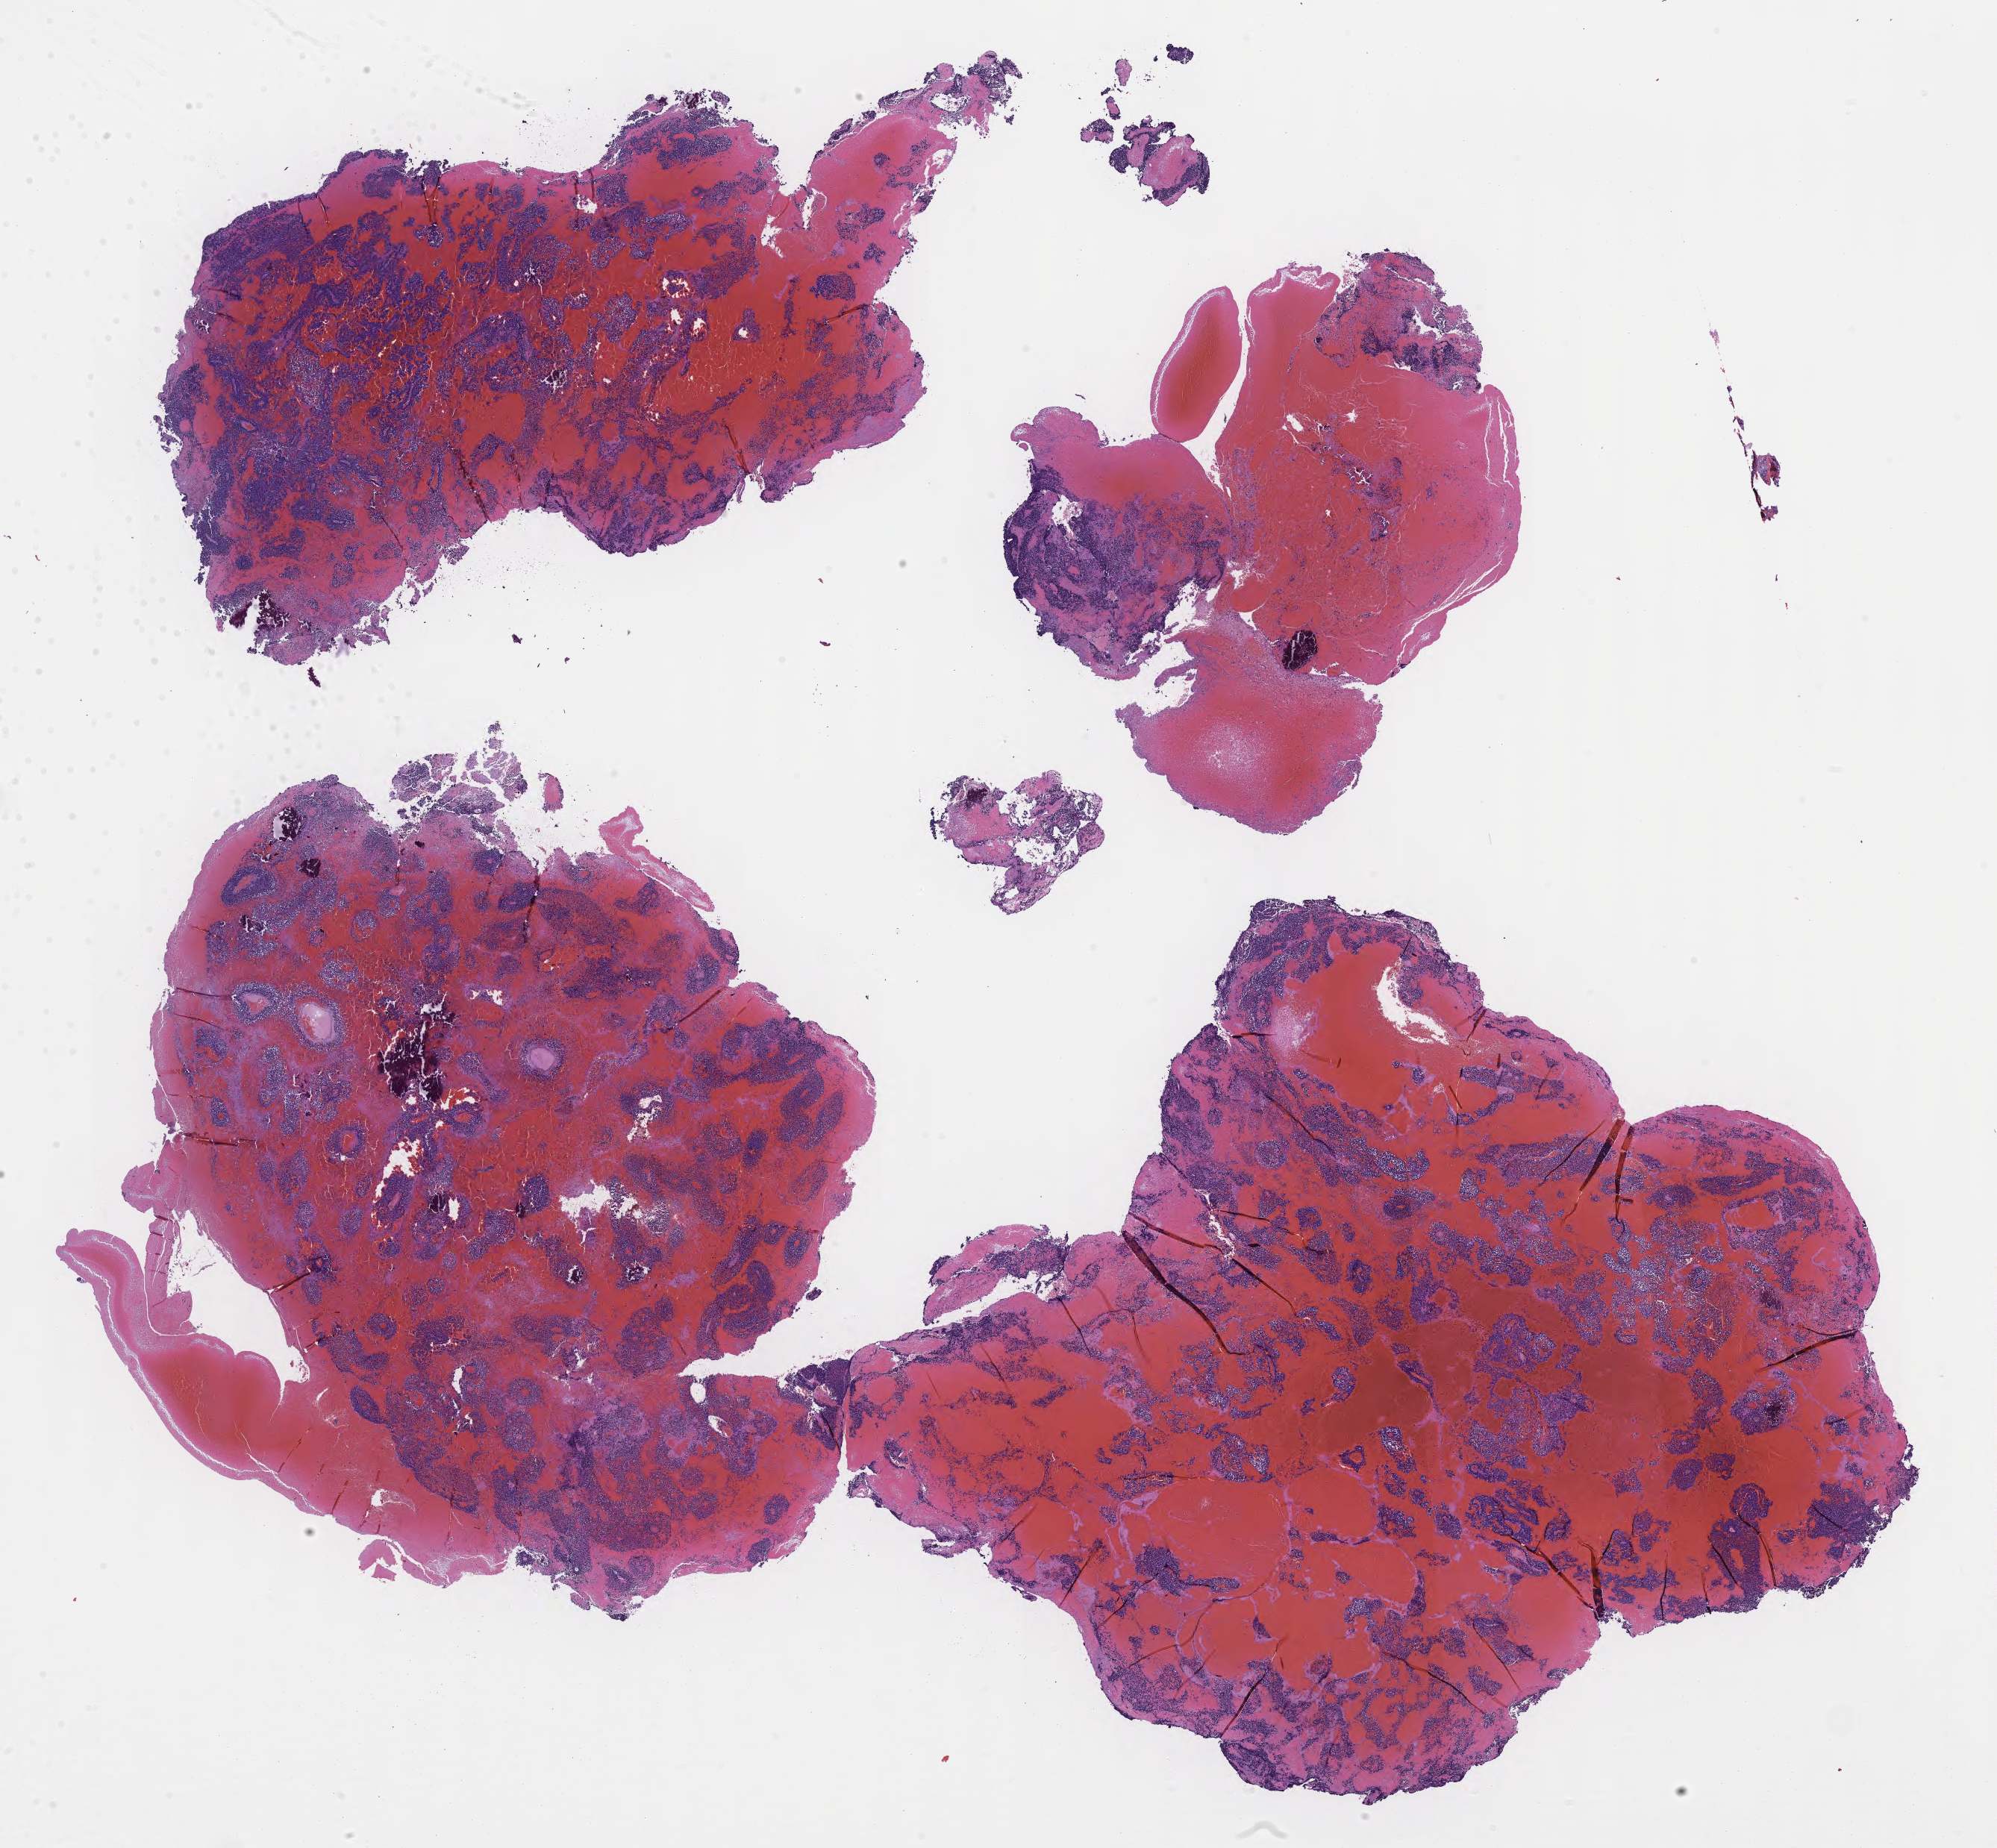
Digitized haematoxylin and eosin-stained section of tumor tissue from the pineal gland, shown as a low-resolution overview of the whole scanned area (about 21.6 x 20.0 mm). Formalin-fixed, paraffin-embedded (FFPE) tissue. Patient male; age 45 months (3 years 9 months).
- recorded diagnosis: Pineoblastoma